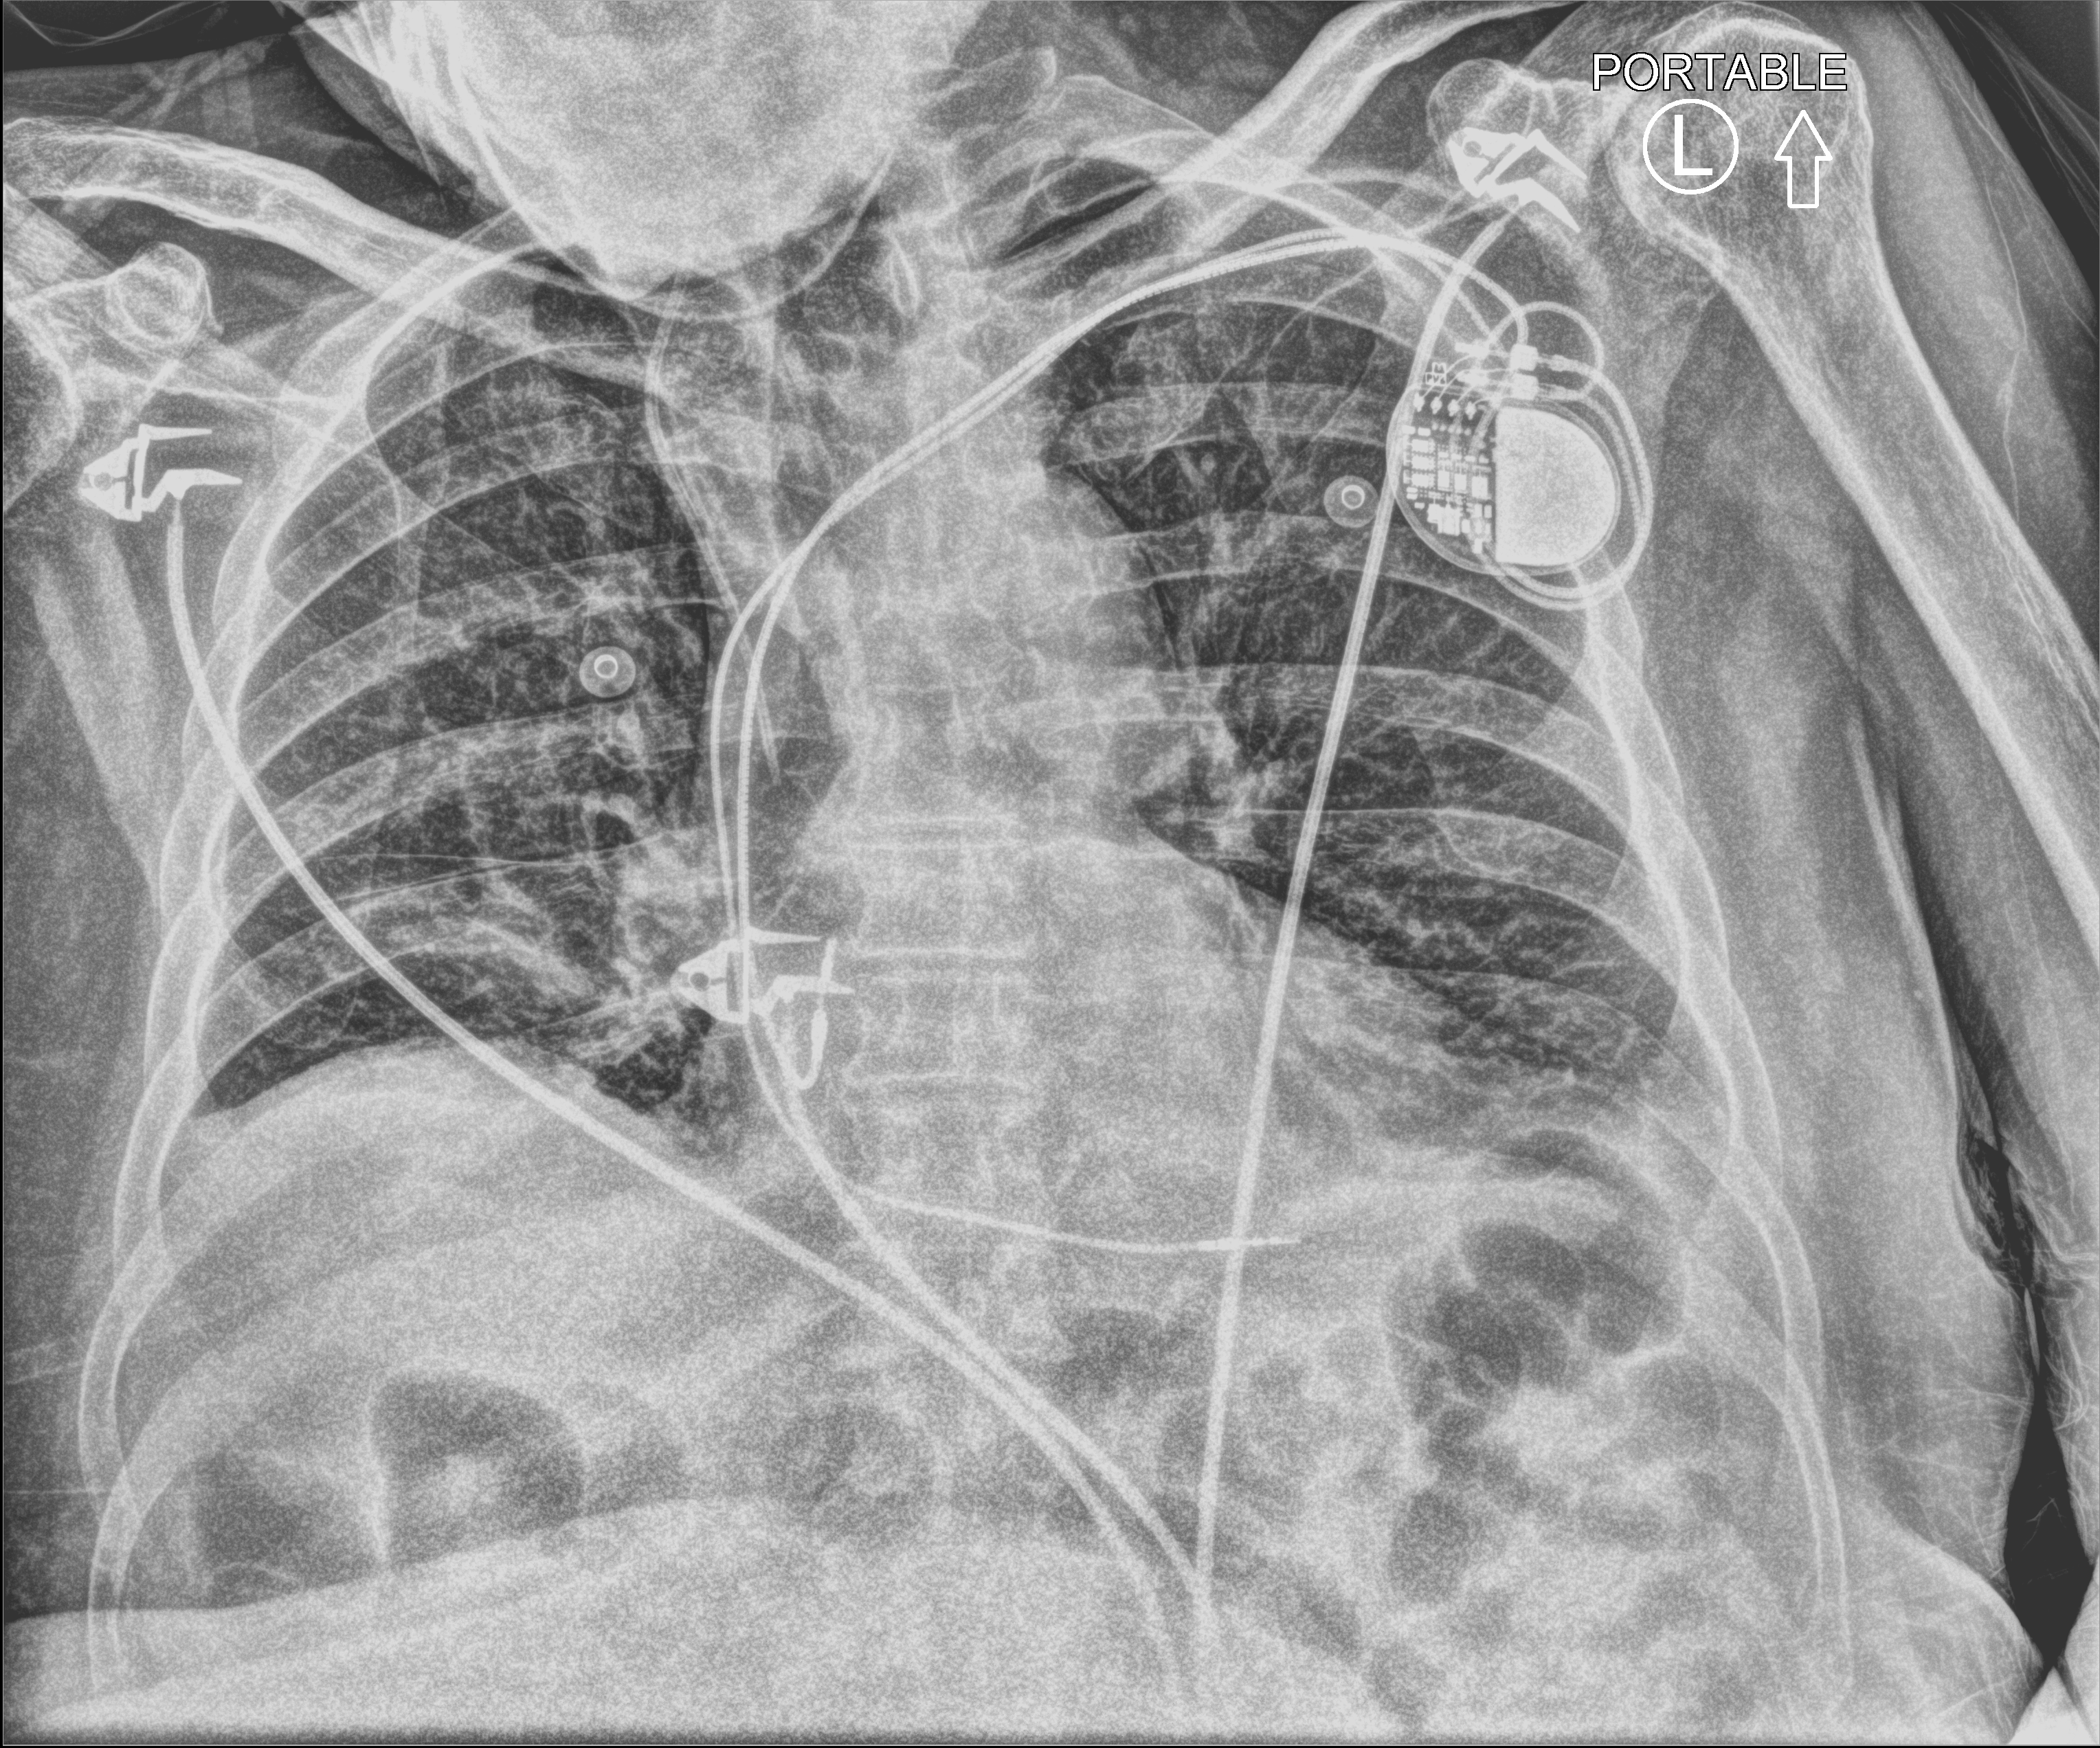
Chest X-ray (portable); anteroposterior (AP) projection. Male patient hospitalised with COVID-19, age 60–74 years.
From the hospital-stay record, not from the radiograph (when in the stay this image was taken is not recorded):
- admitted to intensive care during this hospital stay: no